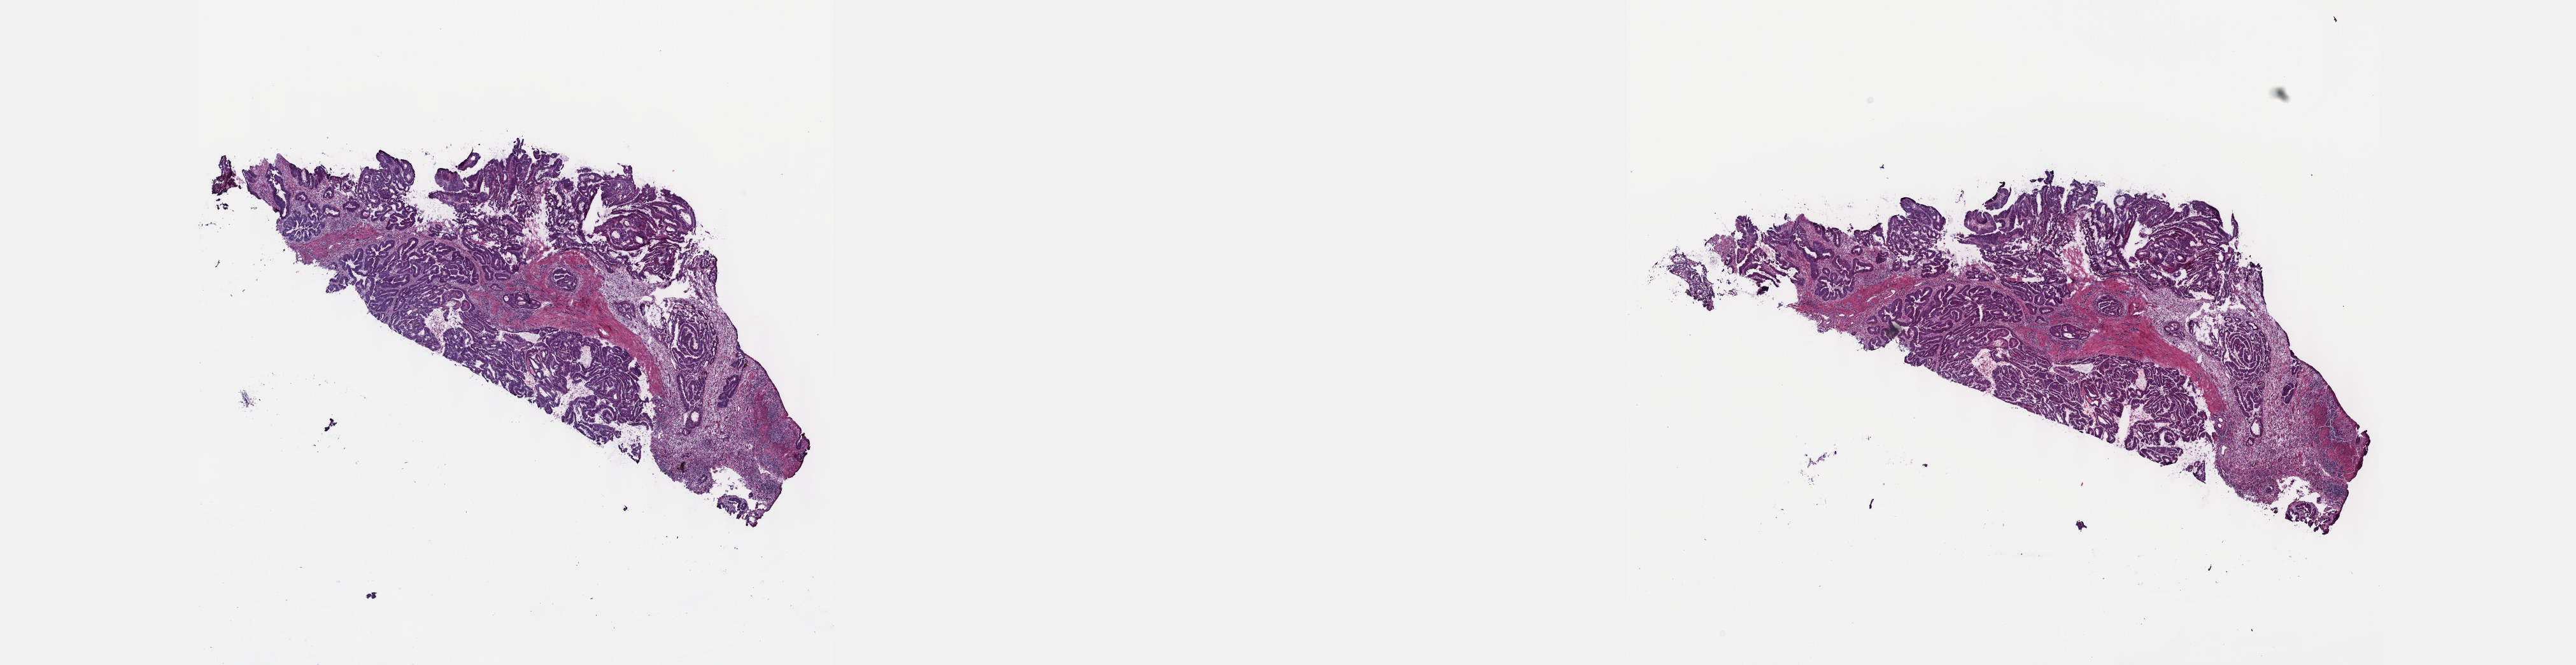
Digitized Hematoxylin and eosin (H&E) stained tissue section (whole slide) — whole scanned area (about 32.7 x 8.4 mm) shown as a low-resolution overview. Frozen section. Primary tumour sample from the colon. Female, age 61 years at initial diagnosis. Slide review estimates, as recorded: tumour cells 60%, tumour nuclei 70%, normal cells 0%, stromal cells 40%, necrosis 0%. Inflammatory infiltration, as recorded: lymphocyte infiltration 0%, monocyte infiltration 0%, neutrophil infiltration 0%.
* lymph nodes positive (case pathology): 0 of 28 examined
* diagnosis: Adenocarcinoma, NOS
* AJCC pathologic stage: I (7th edition)